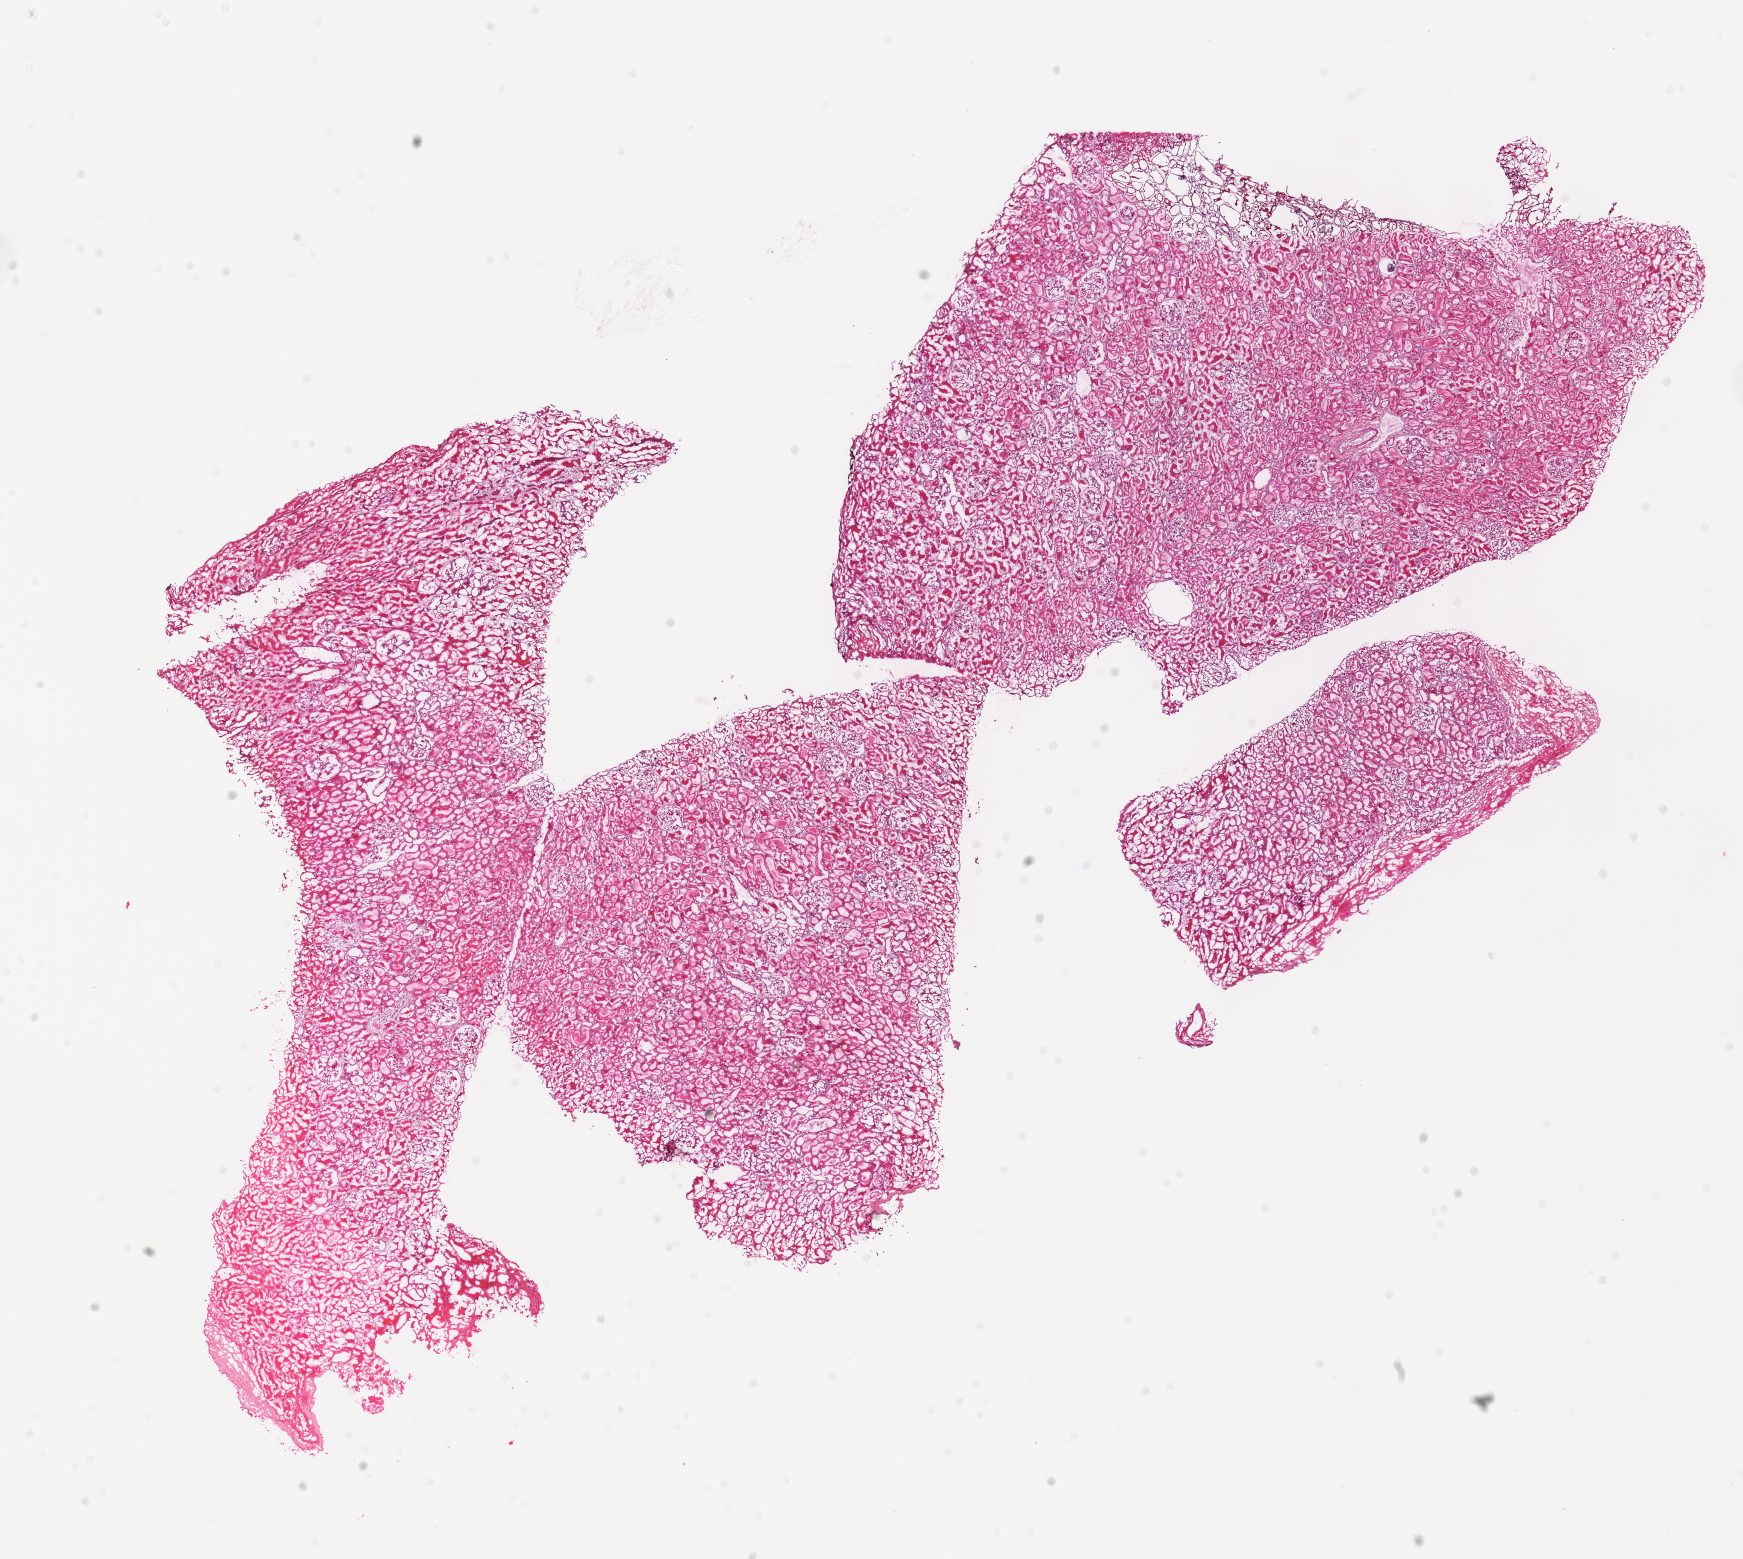
Digitized H&E-stained tissue section (whole slide), a low-resolution overview of the entire scanned area, about 13.7 x 12.3 mm (from a 40x scan). Frozen section from the top of the tissue portion. Kidney, solid tissue normal (non-tumour tissue) sample. Male, age 29 years at initial diagnosis.
• this section: solid tissue normal sample (biorepository sample class)
• patient diagnosis: Renal cell carcinoma, chromophobe type